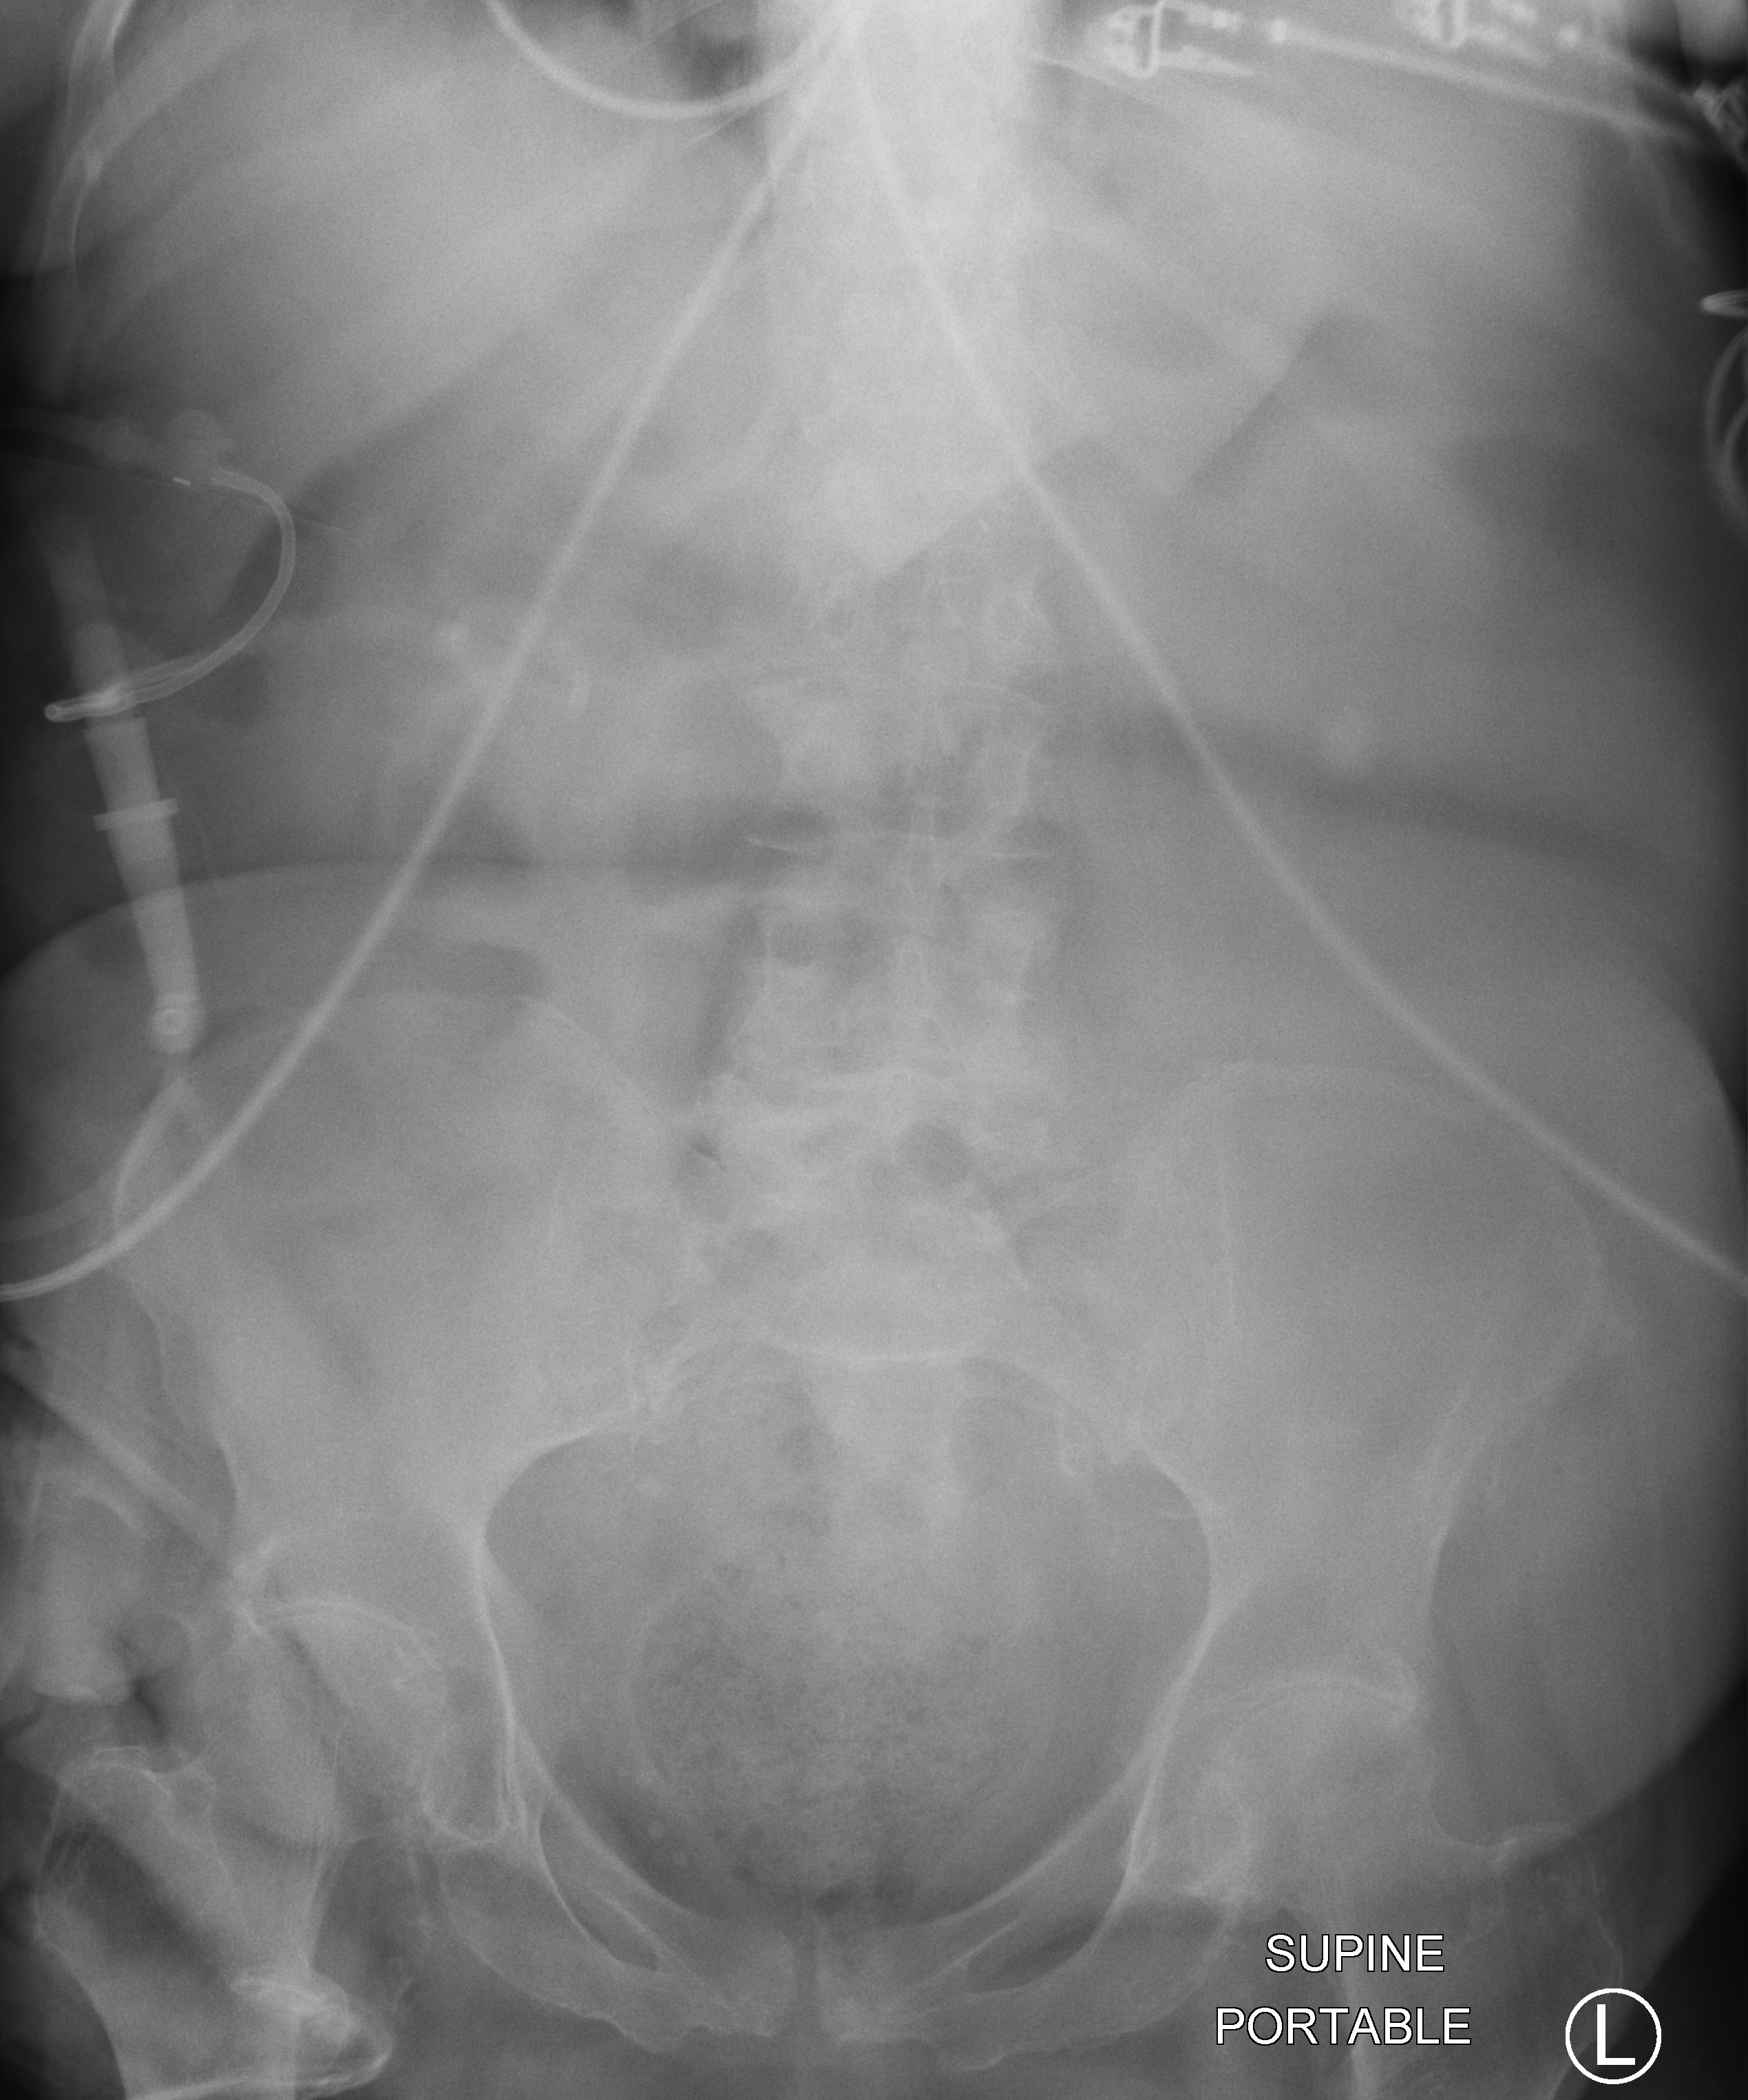
Bedside abdomen radiograph (computed radiography); anteroposterior (AP) projection. Female patient hospitalised with COVID-19, age 75–90 years.
Admission-level facts for this patient (not findings on this image; timing relative to this image not recorded): length of hospital stay: 17 days; mechanically ventilated during this hospital stay: no; chronic kidney disease (admission record): yes.